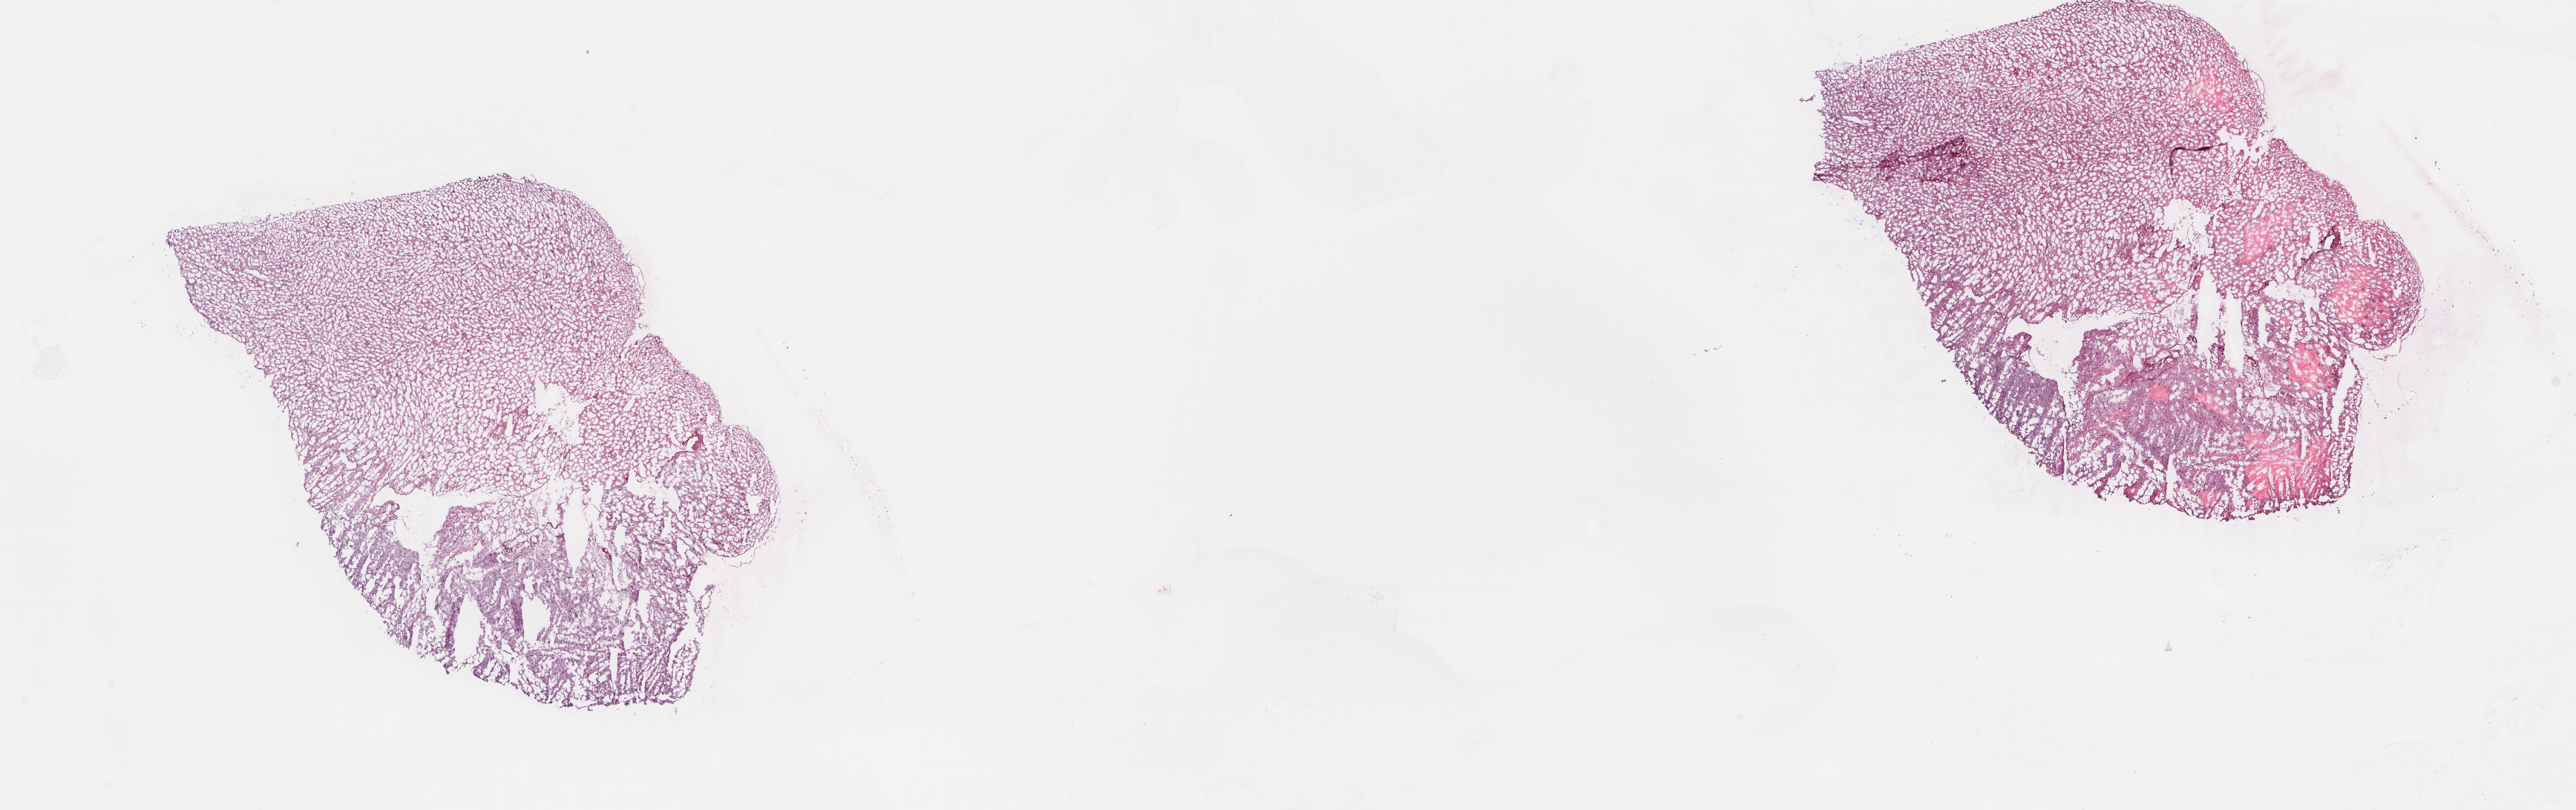
H&E whole-slide image — whole scanned area (about 27.6 x 8.7 mm, from a 40x scan) shown as a low-resolution overview, frozen section from the top of the tissue portion, primary tumour sample from the brain. Female patient; age at initial diagnosis 32 years. Pathologist review of this section (percent, as recorded): tumour cells 40%, tumour nuclei 75%.
Pathologic diagnosis: Mixed glioma.